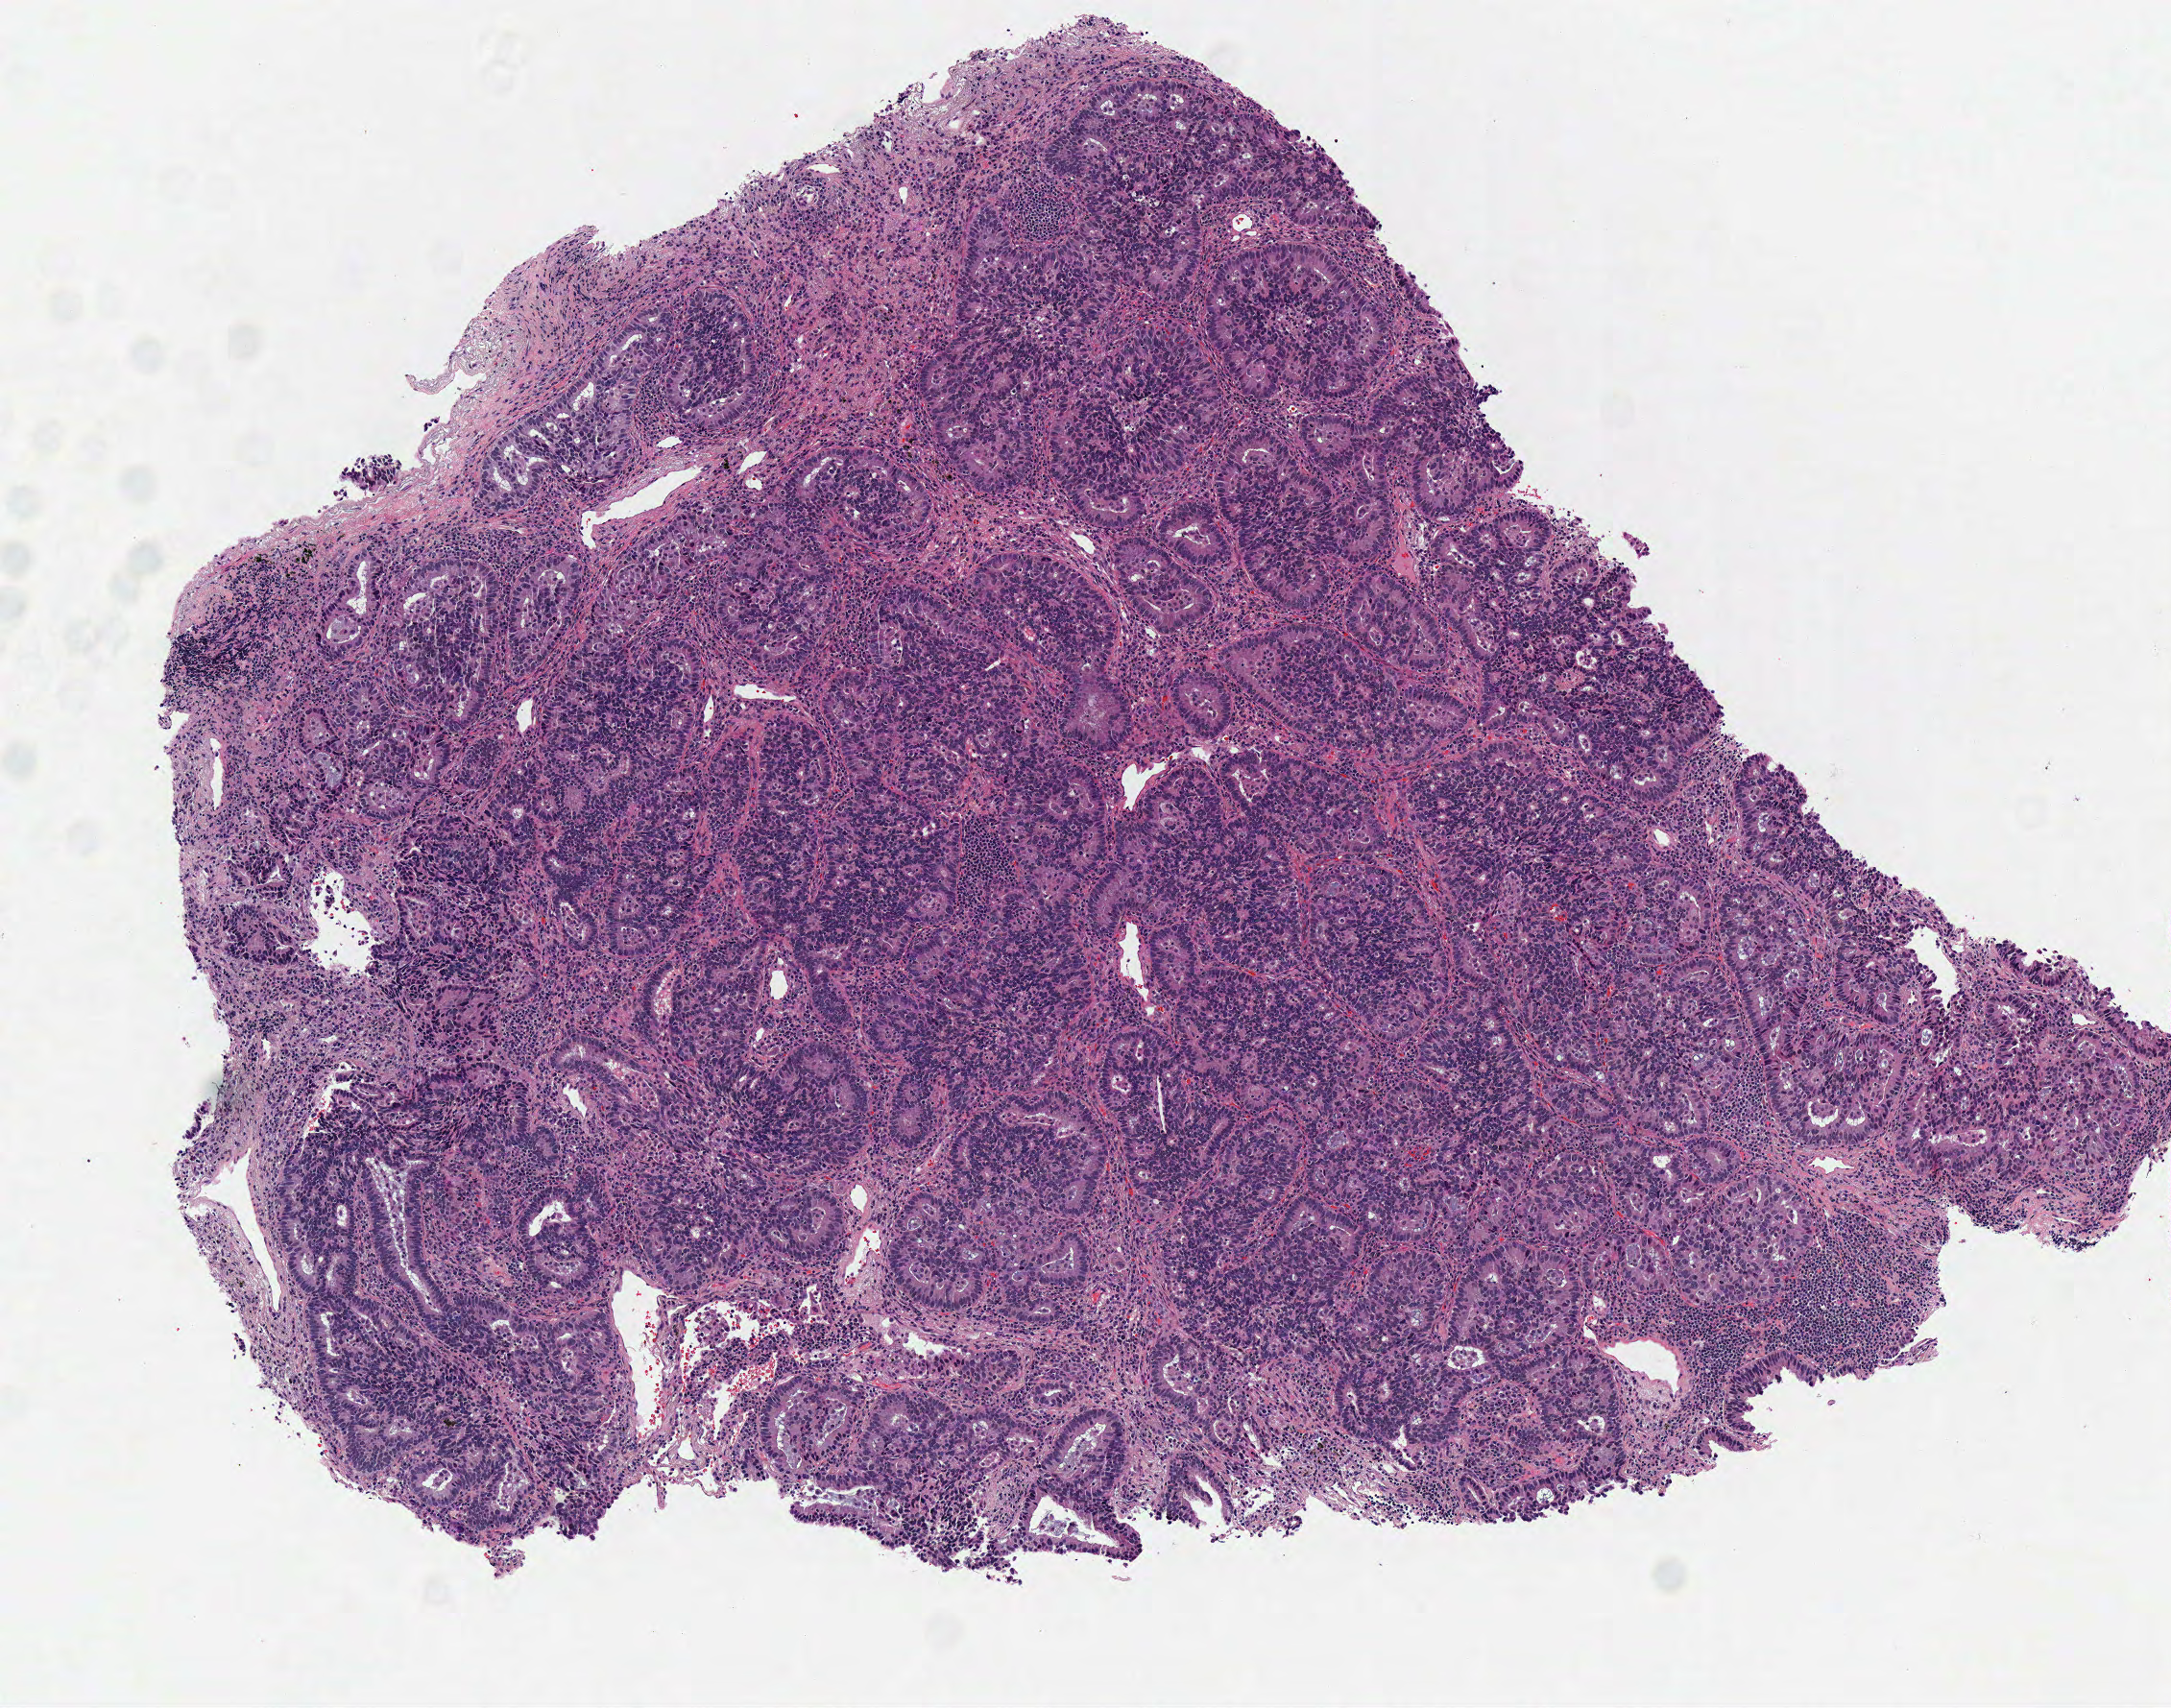
Hematoxylin and eosin (H&E) stained whole-slide image, whole scanned area (about 4.5 x 3.5 mm) shown as a low-resolution overview; frozen section from the top of the tissue portion; primary tumour sample from the lung. Male, age 70 years at initial diagnosis. Slide review estimates, as recorded: tumour cells 90%, tumour nuclei 70%, normal cells 0%, stromal cells 10%, necrosis 0%.
Diagnosis: Adenocarcinoma, NOS (lower lobe, lung). AJCC pathologic stage: IA (7th edition).